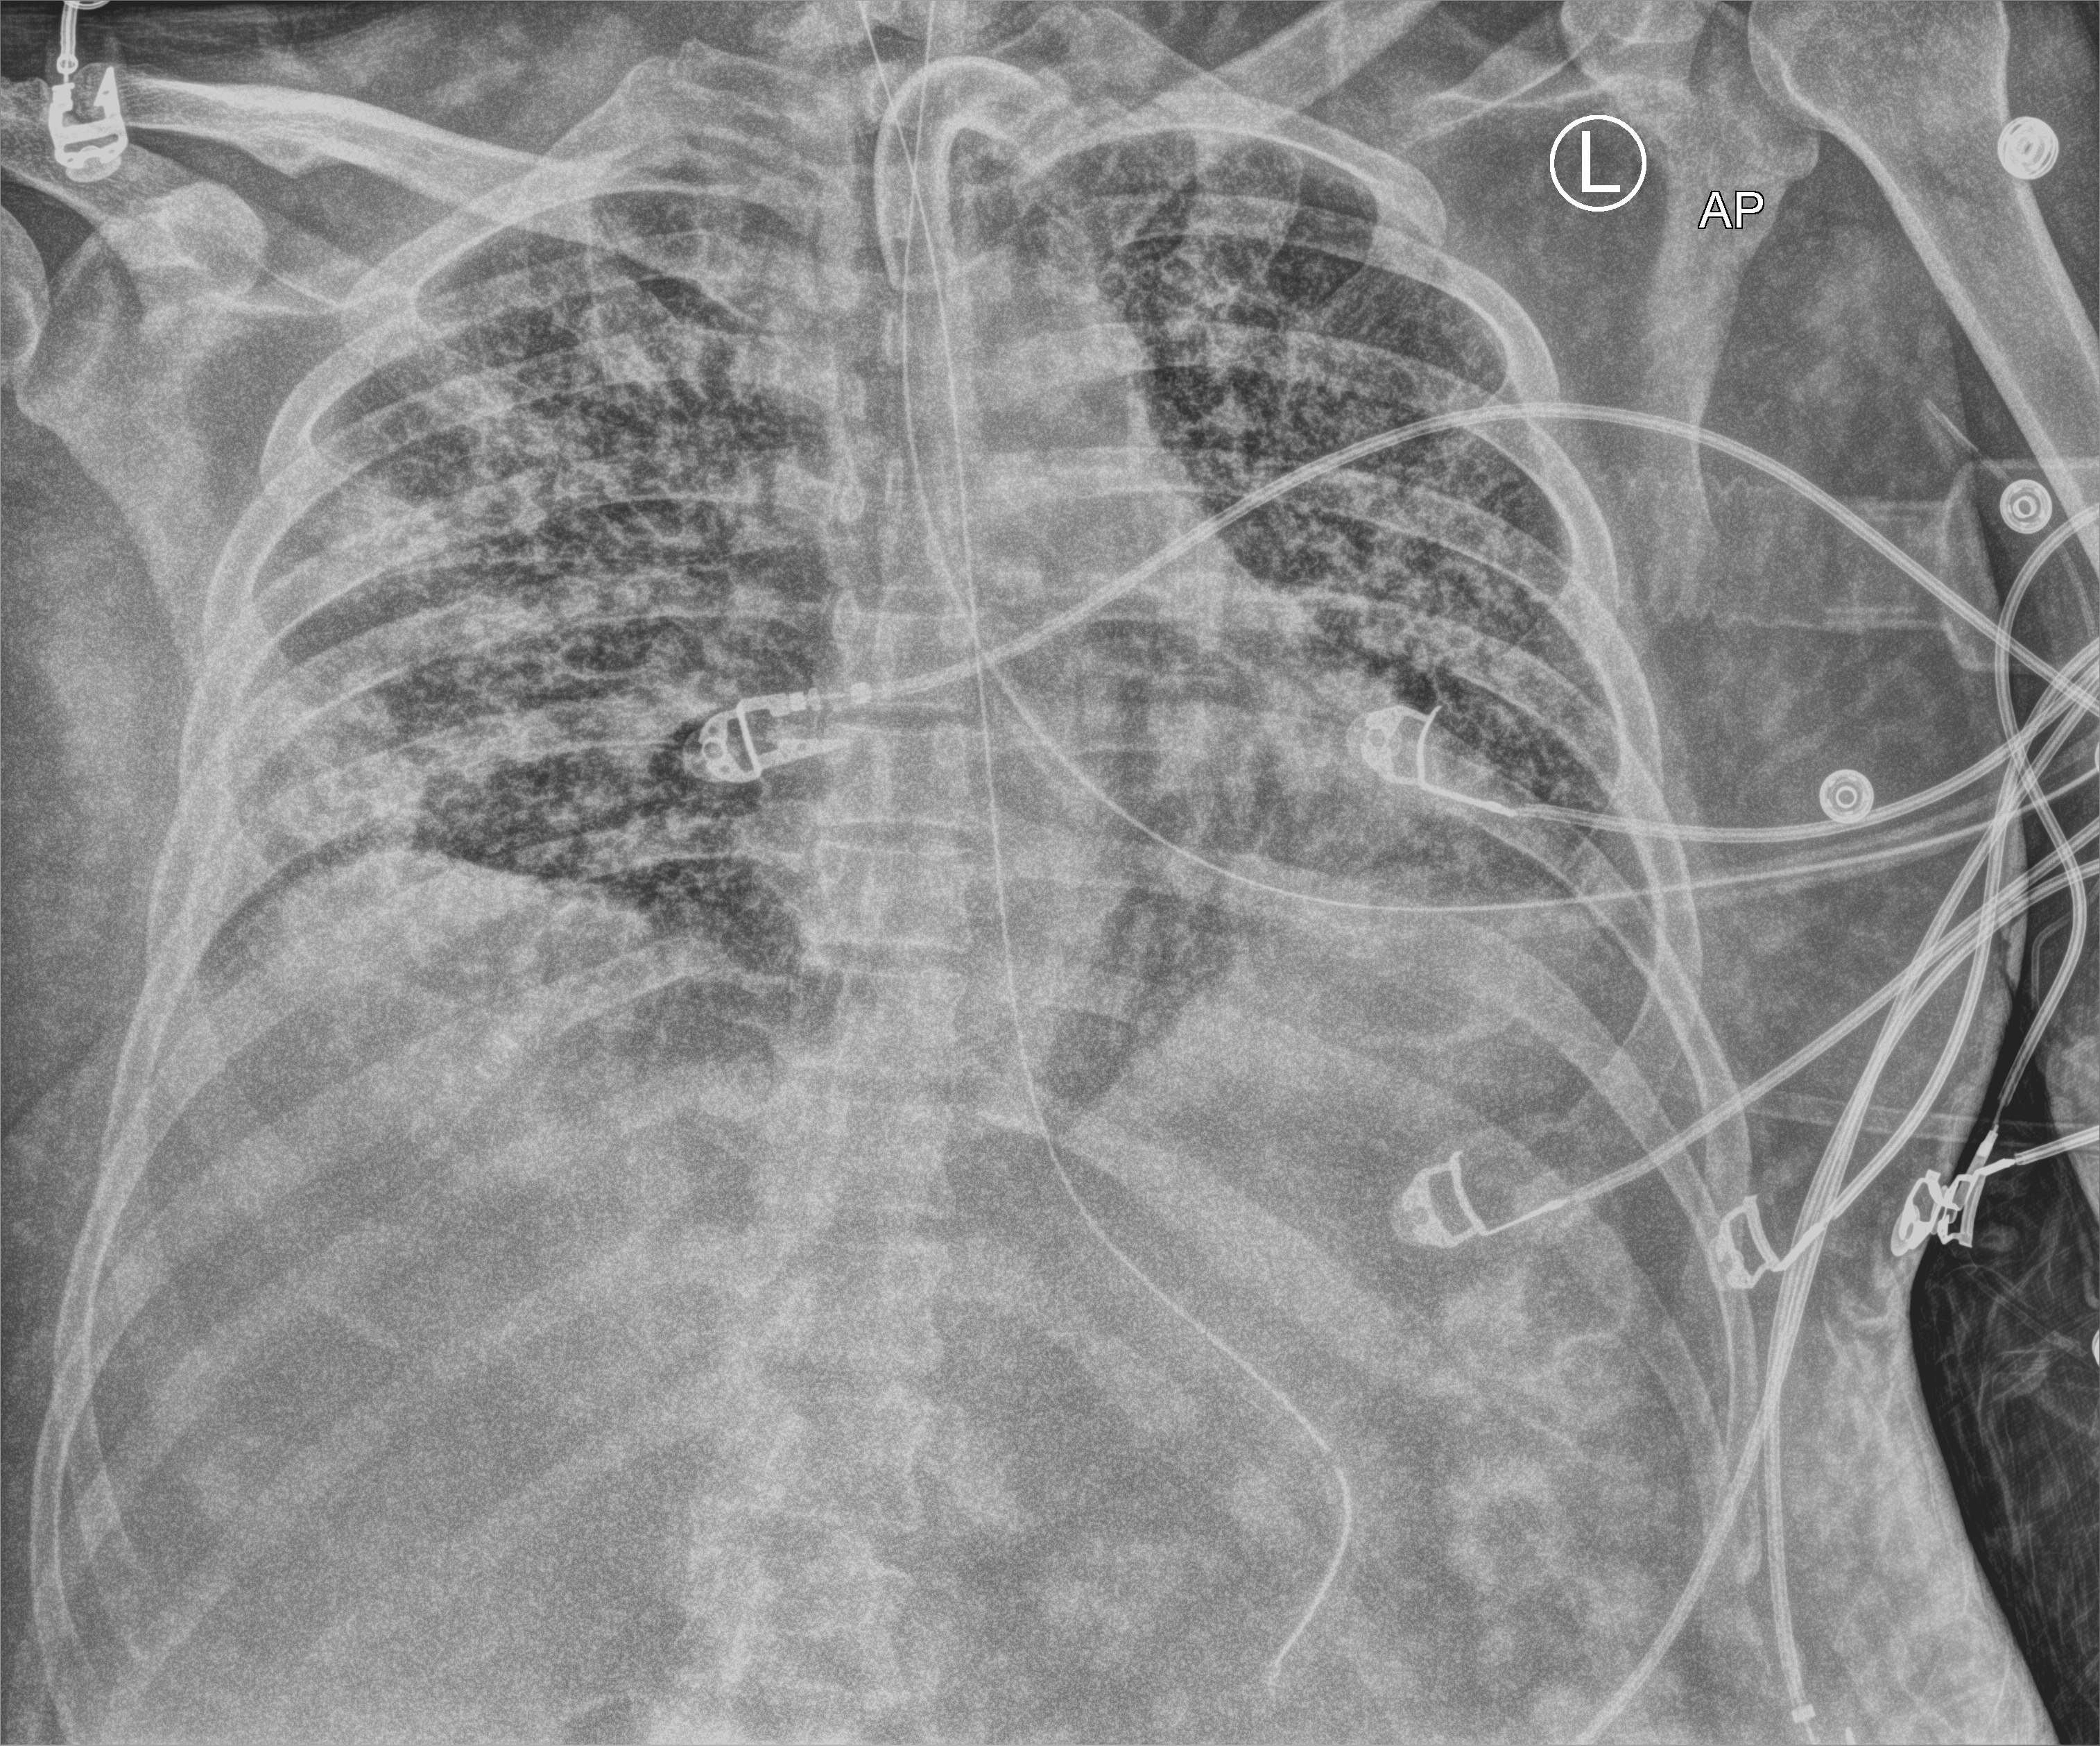
Portable chest radiograph, anteroposterior (AP) projection. Patient hospitalised with COVID-19; male, aged 18–59 years.
Hospital-stay facts (about this admission, not read from this image; timing relative to this image not recorded): mechanically ventilated during this hospital stay: yes; admitted to intensive care during this hospital stay: yes; other chronic lung disease (admission record): no.